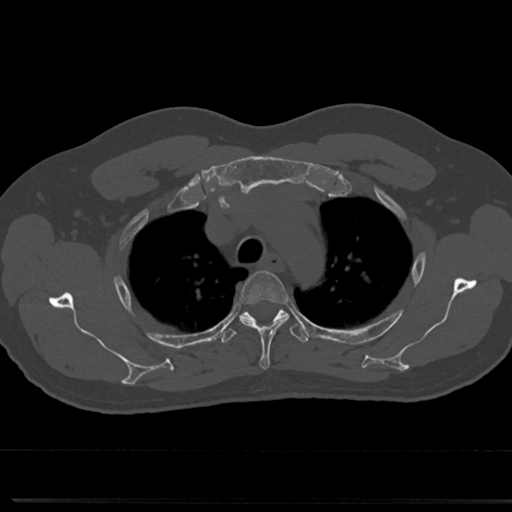
CT including the spine, one axial slice. Slice 573 of 817 in the series (ordered by position). Reconstruction kernel Br40s/3. Bone window (W 1800 / L 400 HU). 0.5 mm slice thickness. 512 × 512 image matrix. Male patient, age 61 years. From the clinical record (not read from this slice): primary cancer: prostate.
Outlined on this slice (semi-automatic segmentation, software-assisted and operator-edited):
- T3 vertebra: bounding box [x1, y1, x2, y2] px = [241, 271, 287, 369]
- T4 vertebra: [220, 301, 310, 345]